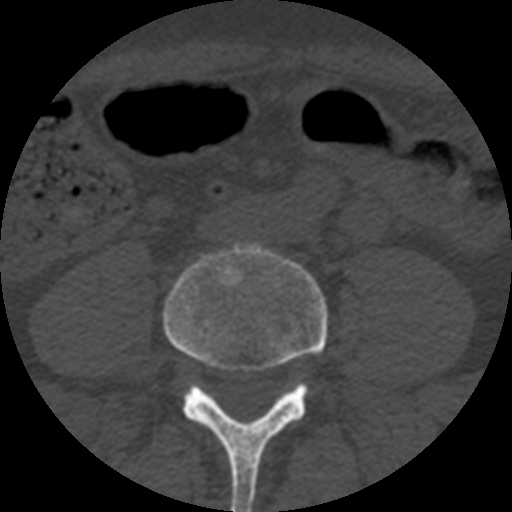
CT including the spine, one axial slice. Slice 87 of 508 in the series (ordered by position). Reconstruction kernel STANDARD. 120 kVp. Bone window (W 1800 / L 400 HU). 1.25 mm slice thickness. 512 × 512 image matrix. Patient age 57 years. From the clinical record (not read from this slice): primary cancer: prostate.
Annotated regions visible in this slice (semi-automatic segmentation, software-assisted and operator-edited):
- L4 vertebra: bounding box (x1, y1, x2, y2) in pixels: (163, 245, 327, 512)